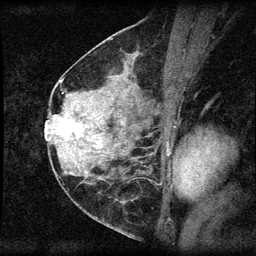
Breast MRI (dynamic contrast-enhanced), one sagittal slice. Slice 28 of 60 in the series (ordered by position). Dynamic contrast-enhanced series, image 2 of 3 at this slice position (ordered by acquisition). 1.5 T. TE 4.2 ms, TR 8.2 ms. 256 × 256 image matrix, field of view 180 × 180 mm. Patient: female, 45 years.
Structures marked on this image (semi-automatic segmentation, software-assisted and operator-edited):
- analysis volume of interest (the breast-tissue region the enhancement analysis was run in; not a lesion): box from (x=55, y=110) to (x=94, y=148) px
- tumour enhancement mask (voxels above the 70 % enhancement threshold inside the analysis volume of interest): (x=59, y=118)–(x=80, y=138)